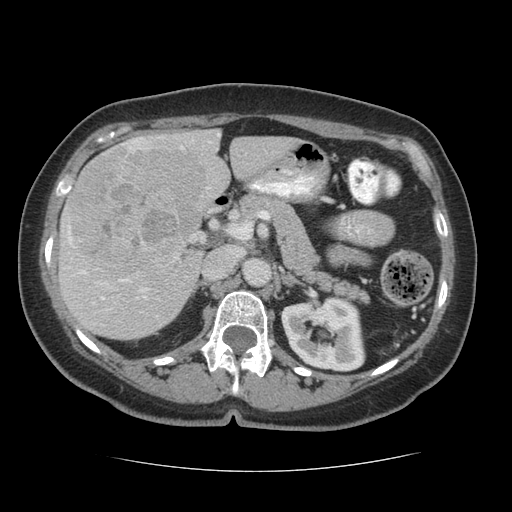
Contrast-enhanced abdominal CT (liver protocol), one axial slice; slice 32 of 75 in the series (ordered by position); reconstruction kernel STANDARD; soft-tissue window (W 400 / L 40 HU); 512 × 512 image matrix. From the clinical record (not read from this slice): diagnosis: hepatocellular carcinoma (patient treated with transarterial chemoembolisation; whether this scan precedes or follows treatment is not stated here); TNM stage (as recorded): Stage-I; Child-Pugh class: A; tumour nodularity: uninodular.
Outlined on this slice (semi-automatic segmentation, software-assisted and operator-edited):
- liver parenchyma outside the tumour (the mass and vessels are separate outlines, so this box may not span the whole liver): bounding box <58,128,298,338> (left, top, right, bottom; pixels)
- mass: <66,148,206,287>
- liver vessels: <68,133,220,304>